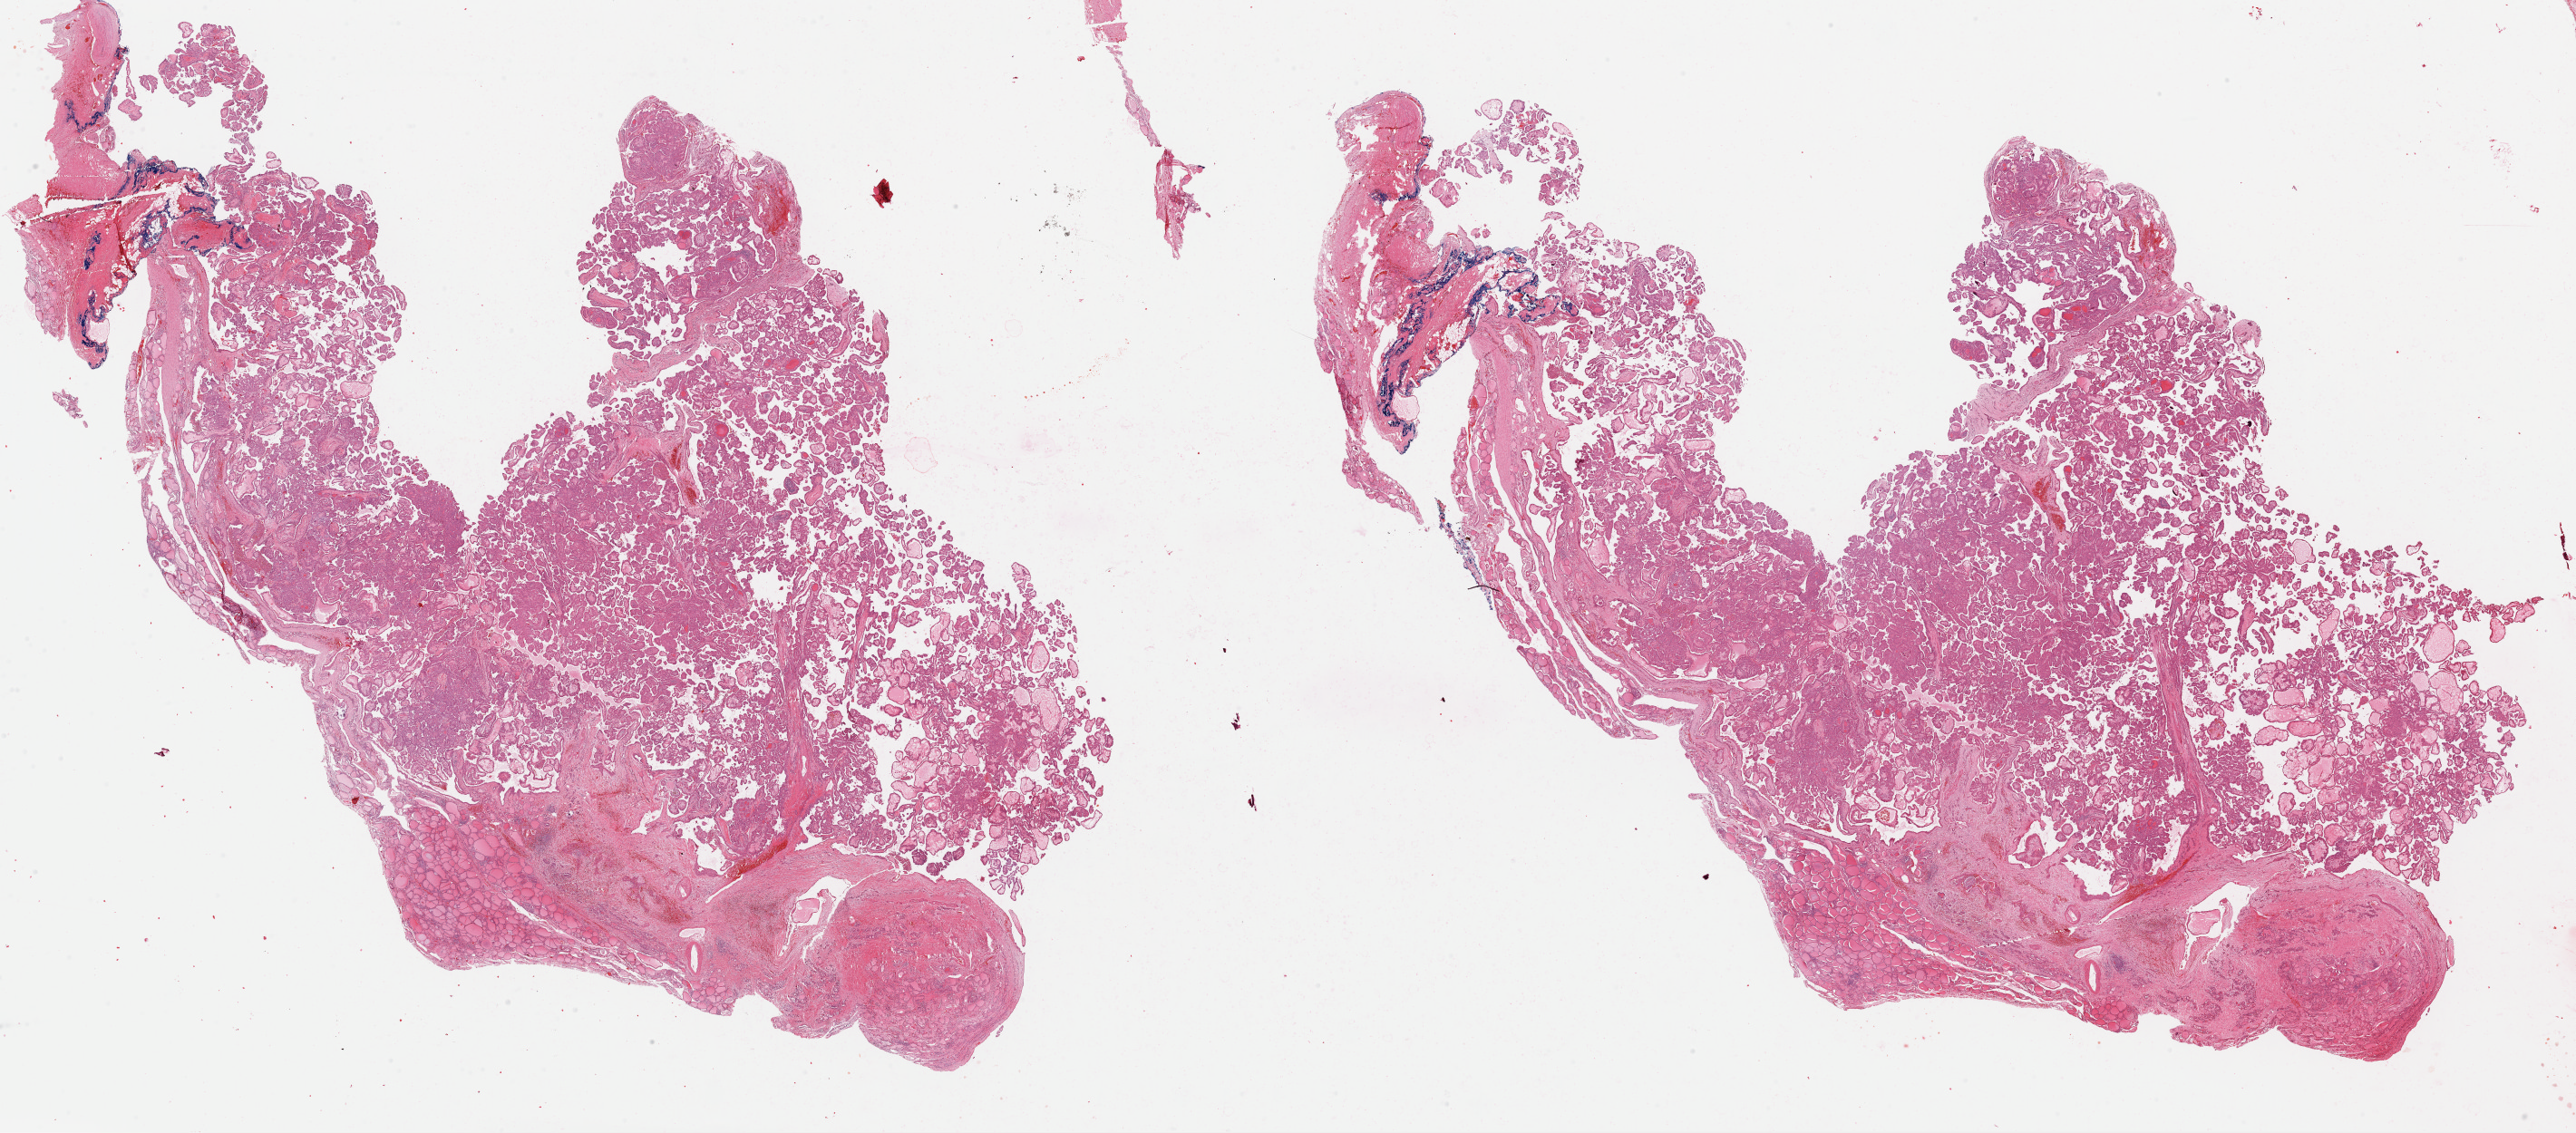
Hematoxylin and eosin (H&E) stained whole-slide image — shown as a low-resolution overview of the whole scanned area (about 44.9 x 19.7 mm, slide scanned at 40x); formalin-fixed paraffin-embedded (FFPE) diagnostic section; sample: primary tumour, thyroid. Patient: female, age at initial diagnosis 49 years.
TNM: T2 N0 M0. AJCC pathologic stage: II. Pathologic diagnosis: Papillary adenocarcinoma, NOS (thyroid gland).